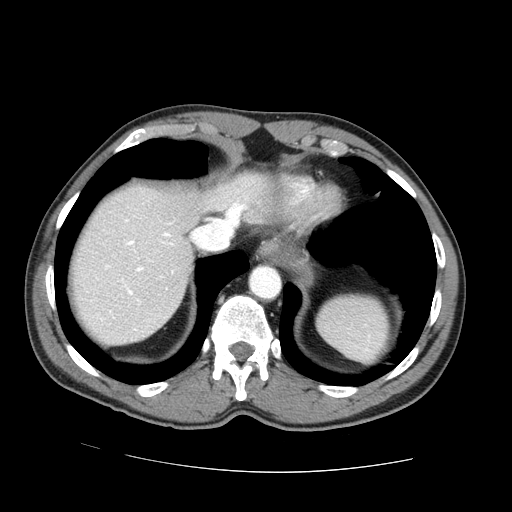
Contrast-enhanced abdominal CT (liver protocol), one axial slice. Slice 61 of 73 in the series (ordered by position). 100 kVp. One of 2 acquisitions stored at this slice position. Soft-tissue window (W 400 / L 40 HU). 2.5 mm slice thickness. 512 × 512 image matrix, field of view 380 × 380 mm. From the clinical record (not read from this slice): diagnosis: hepatocellular carcinoma (patient treated with transarterial chemoembolisation; whether this scan precedes or follows treatment is not stated here); TNM stage (as recorded): Stage-IVA; Child-Pugh class: A; tumour differentiation: no biopsy; tumour nodularity: uninodular.
Structures marked on this image (semi-automatically segmented with operator editing):
- abdominal aorta: bounding box (x1, y1, x2, y2) in pixels: (251, 266, 280, 299)
- liver parenchyma outside the tumour (the mass and vessels are separate outlines, so this box may not span the whole liver): (72, 176, 244, 344)
- liver vessels: (127, 233, 172, 295)